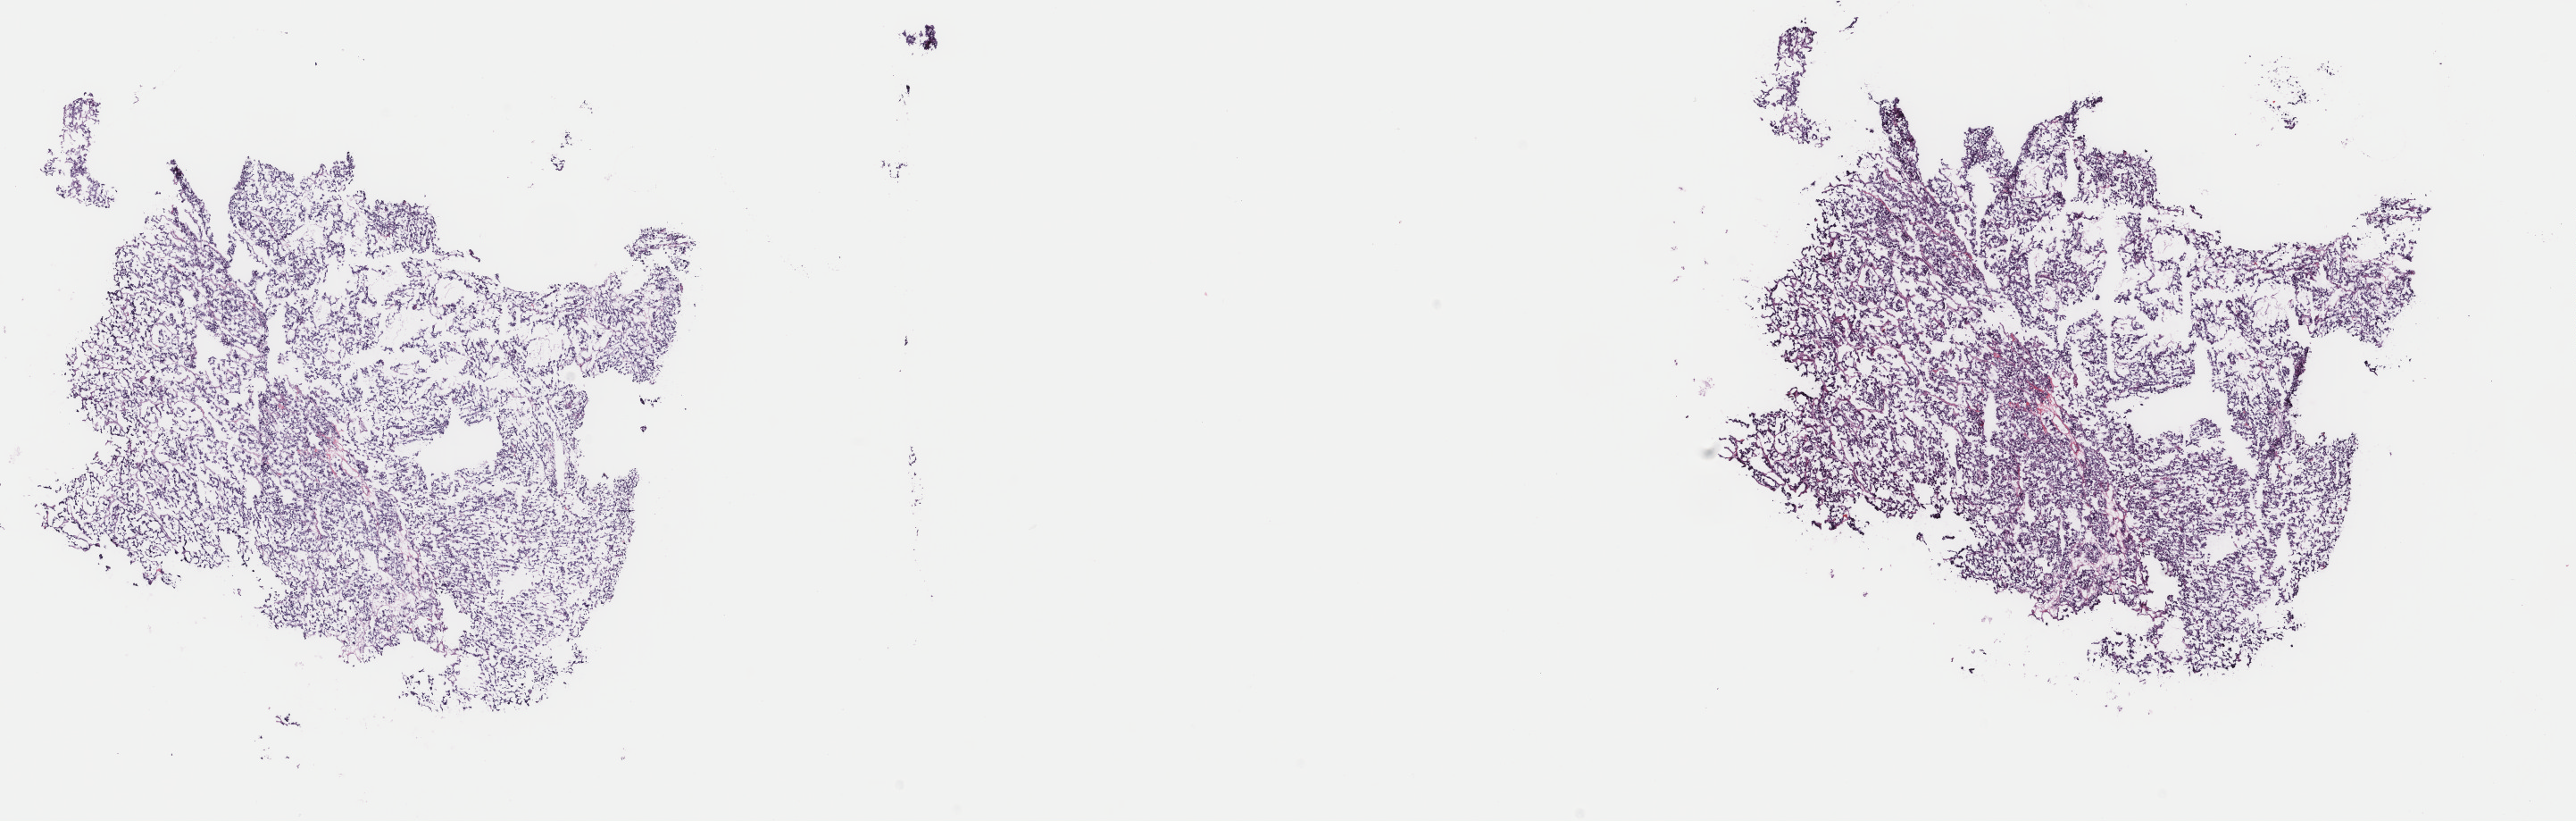
Digitized Hematoxylin and eosin (H&E) stained tissue section (whole slide) — a low-resolution overview of the entire scanned area, about 22.9 x 7.3 mm (acquisition: 40x scan), frozen section from the top of the tissue portion, sample: primary tumour, adrenal gland. Patient: female, age at initial diagnosis 71 years. Slide review estimates, as recorded: tumour cells 90%, tumour nuclei 90%, normal cells 0%, stromal cells 5%, necrosis 5%. Infiltration values recorded for this section: lymphocyte infiltration 40%, monocyte infiltration 20%, neutrophil infiltration 20%.
* pathologic diagnosis: Pheochromocytoma, NOS